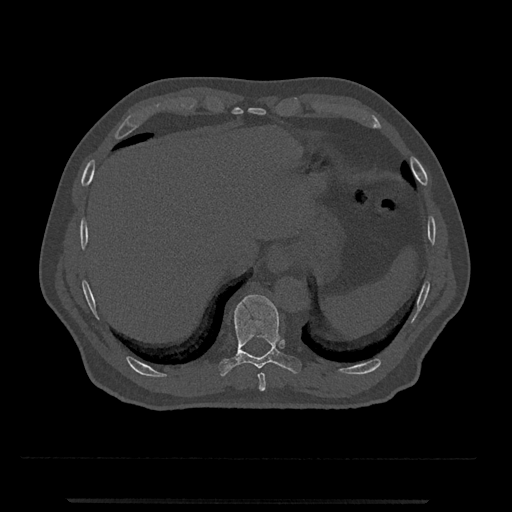
CT including the spine, one axial slice. Position 524 of 797 along the scan axis. Reconstruction kernel Br40s/3. 120 kVp. Bone window (W 1800 / L 400 HU). 0.5 mm slice thickness. 512 × 512 image matrix, field of view 419 × 419 mm. Patient: male, 63 years. From the clinical record (not read from this slice): primary cancer: prostate.
Structures marked on this image (semi-automatically segmented with operator editing):
- T10 vertebra: bounding box [x1, y1, x2, y2] px = [218, 295, 302, 377]
- T9 vertebra: [258, 373, 266, 392]